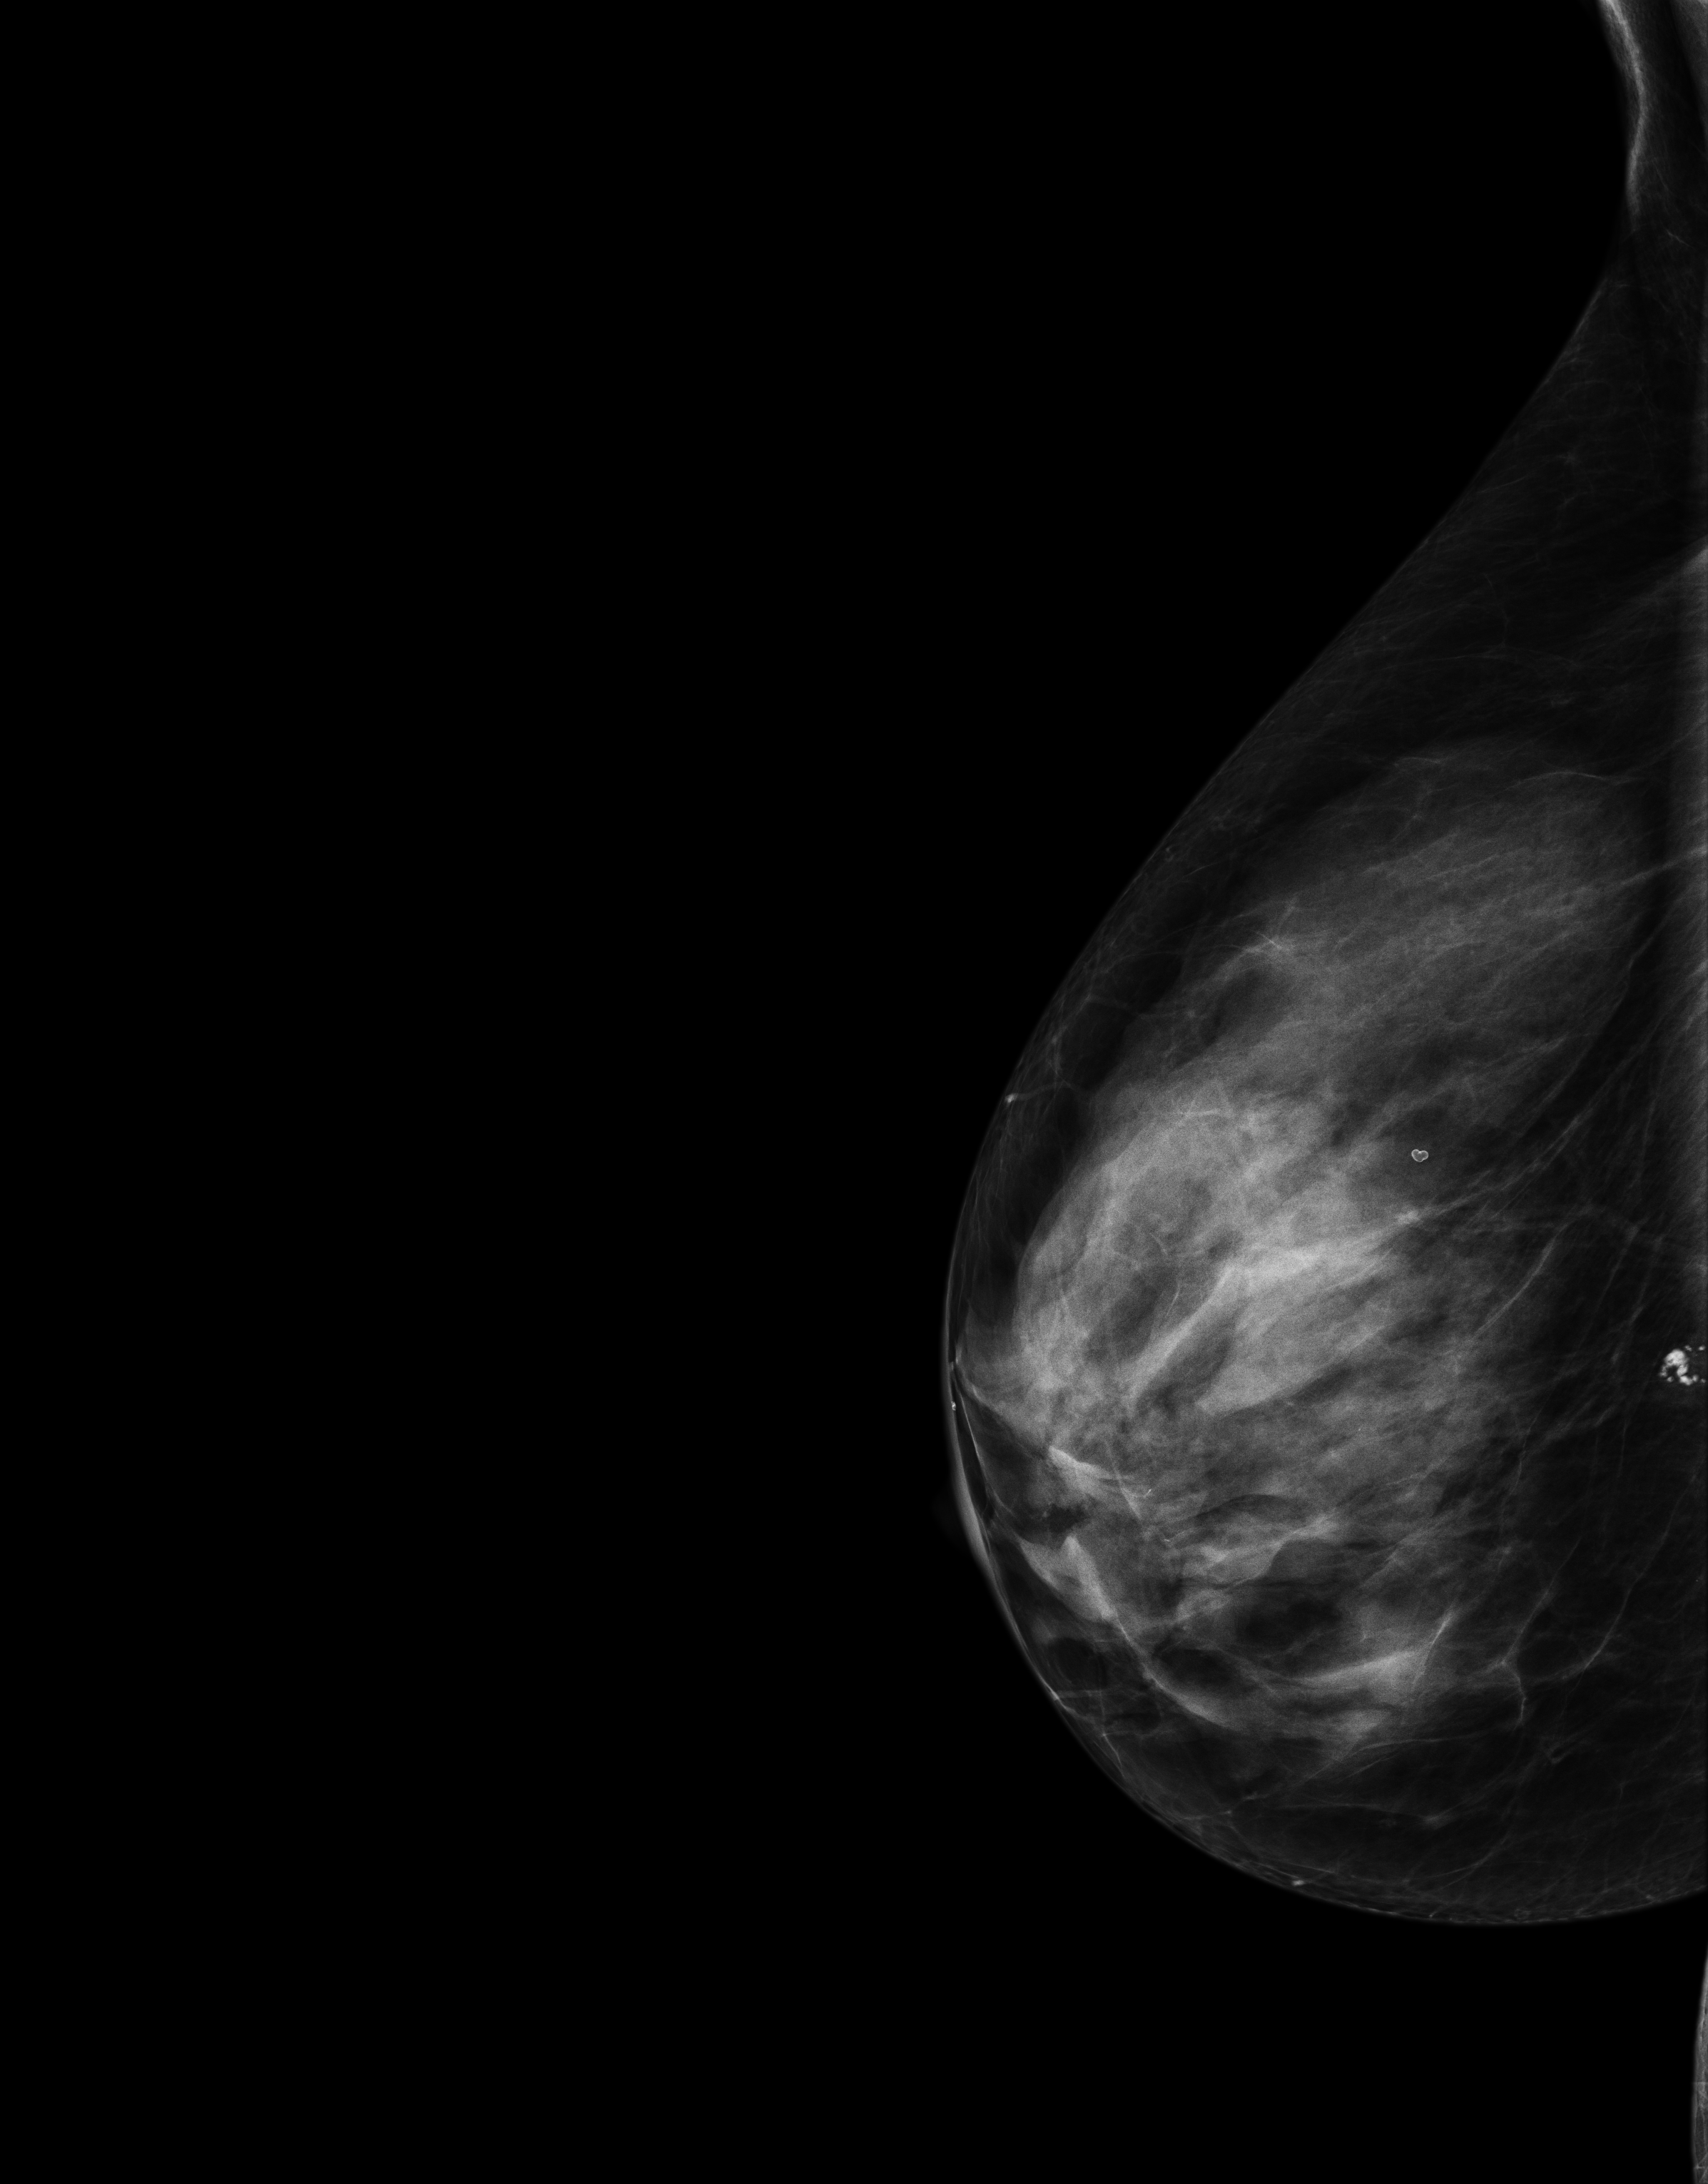
Screening examination, compressed breast thickness 53 mm, system: Senographe Essential ADS_56.21.3. Female patient, age 61 years.
Image type: full-field digital mammogram. Breast: right. Projection: laterally exaggerated craniocaudal (XCCL) view.